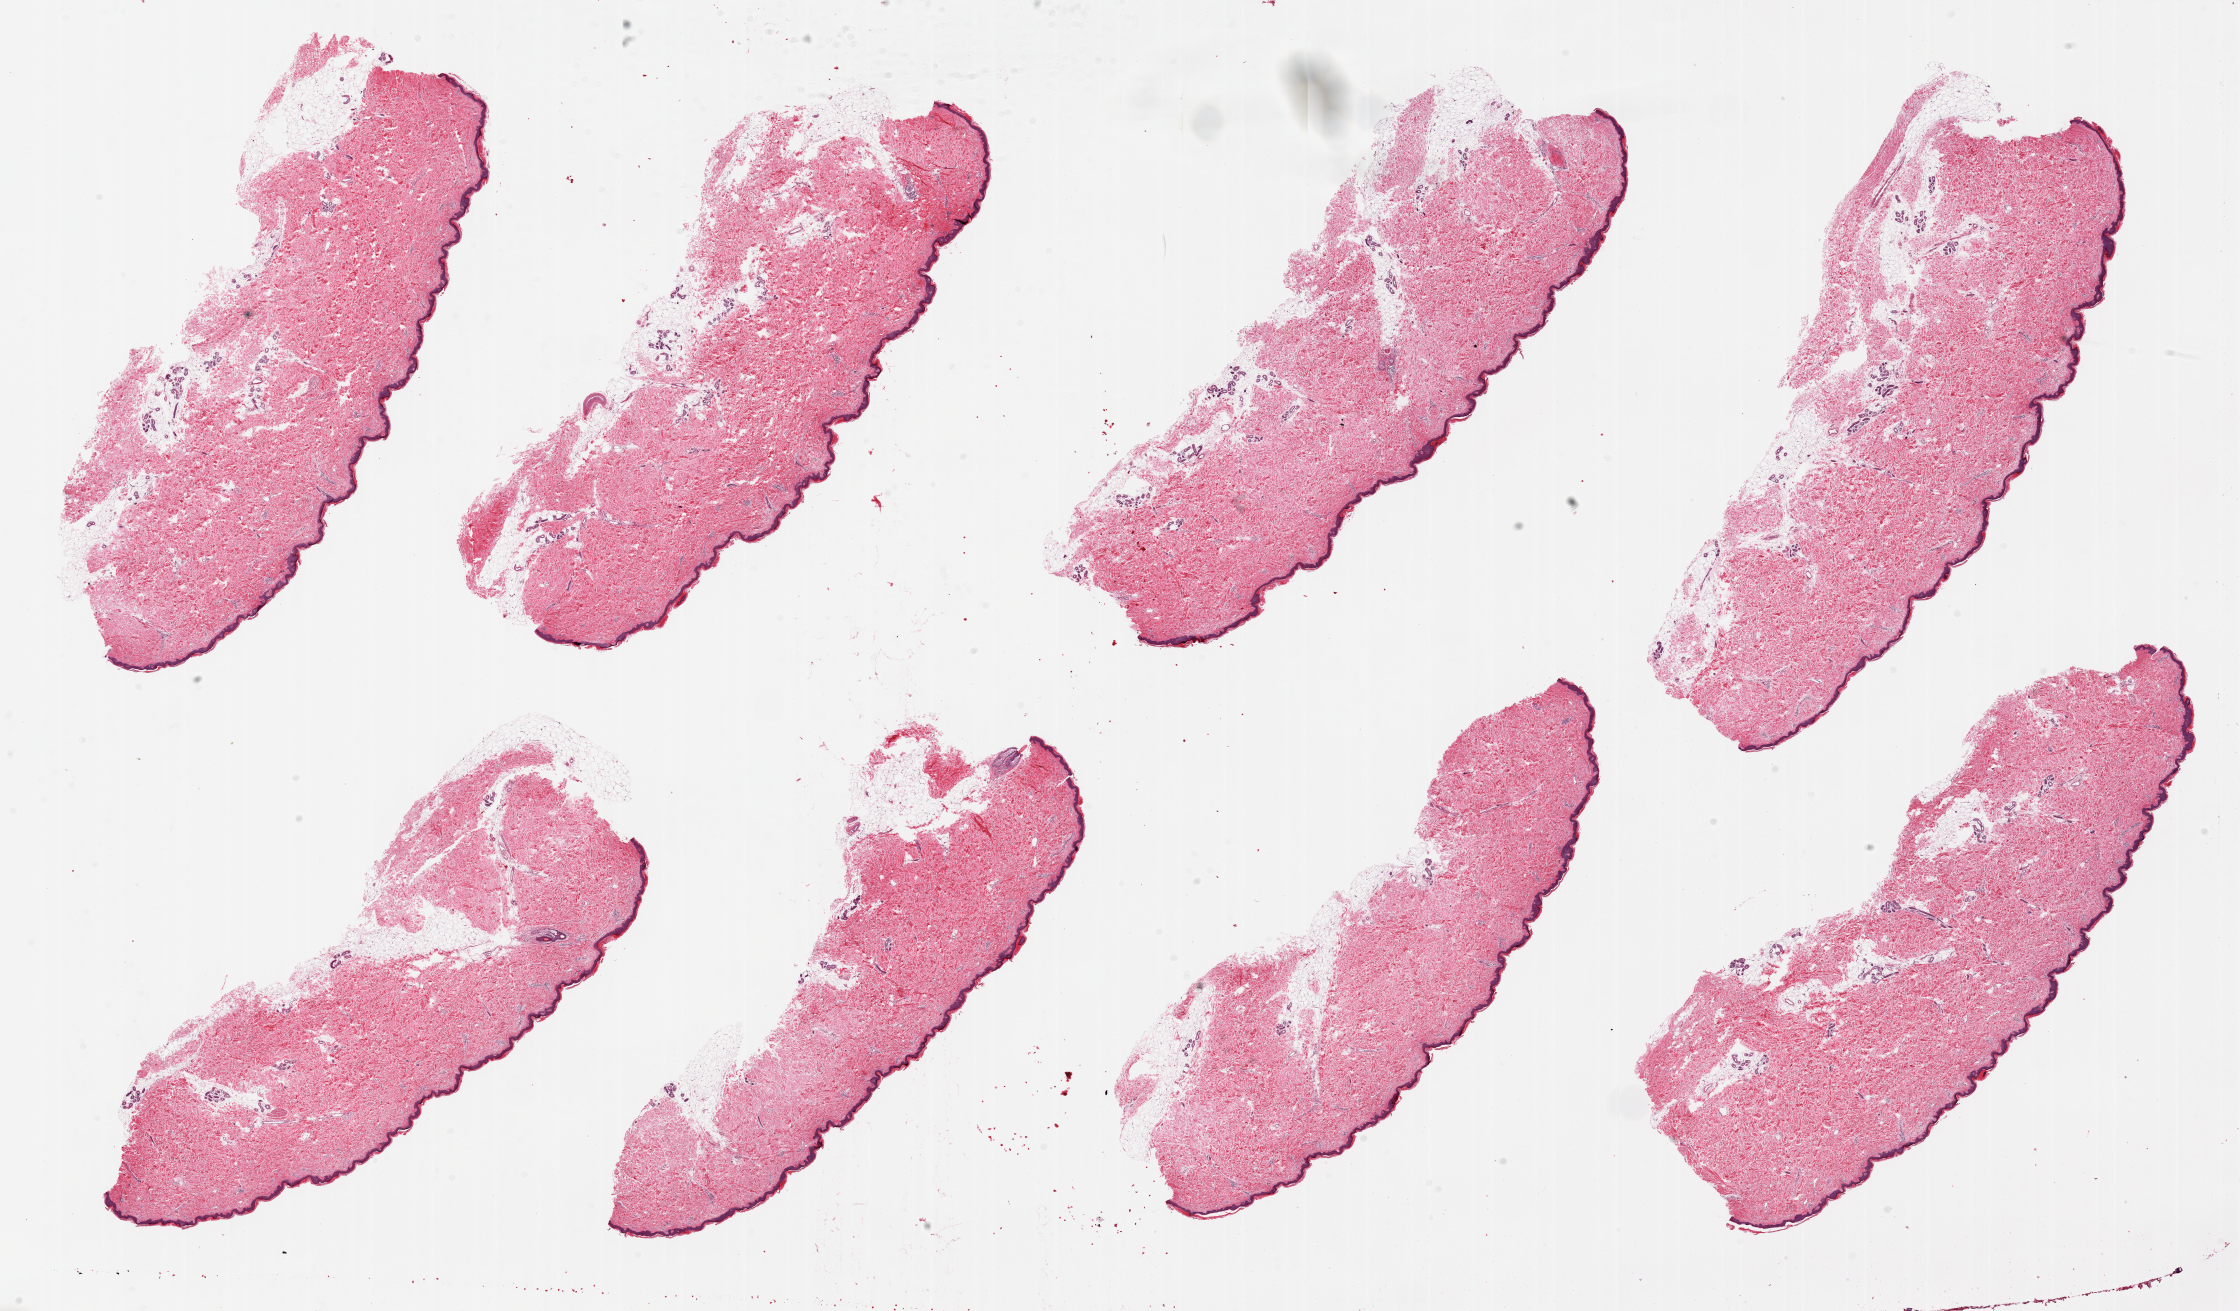
Digitized hematoxylin and eosin (H&E)-stained section, a low-resolution overview of the entire scanned area, about 35.4 x 20.7 mm. PAXgene-fixed, paraffin-embedded tissue. Section of skin of lower leg (target tissue). Tissue donor sample. Female donor.
Reviewer comment on this tissue sample: 8 pieces, up to 11x5mm; squamous epithelium is ~2% thickness.